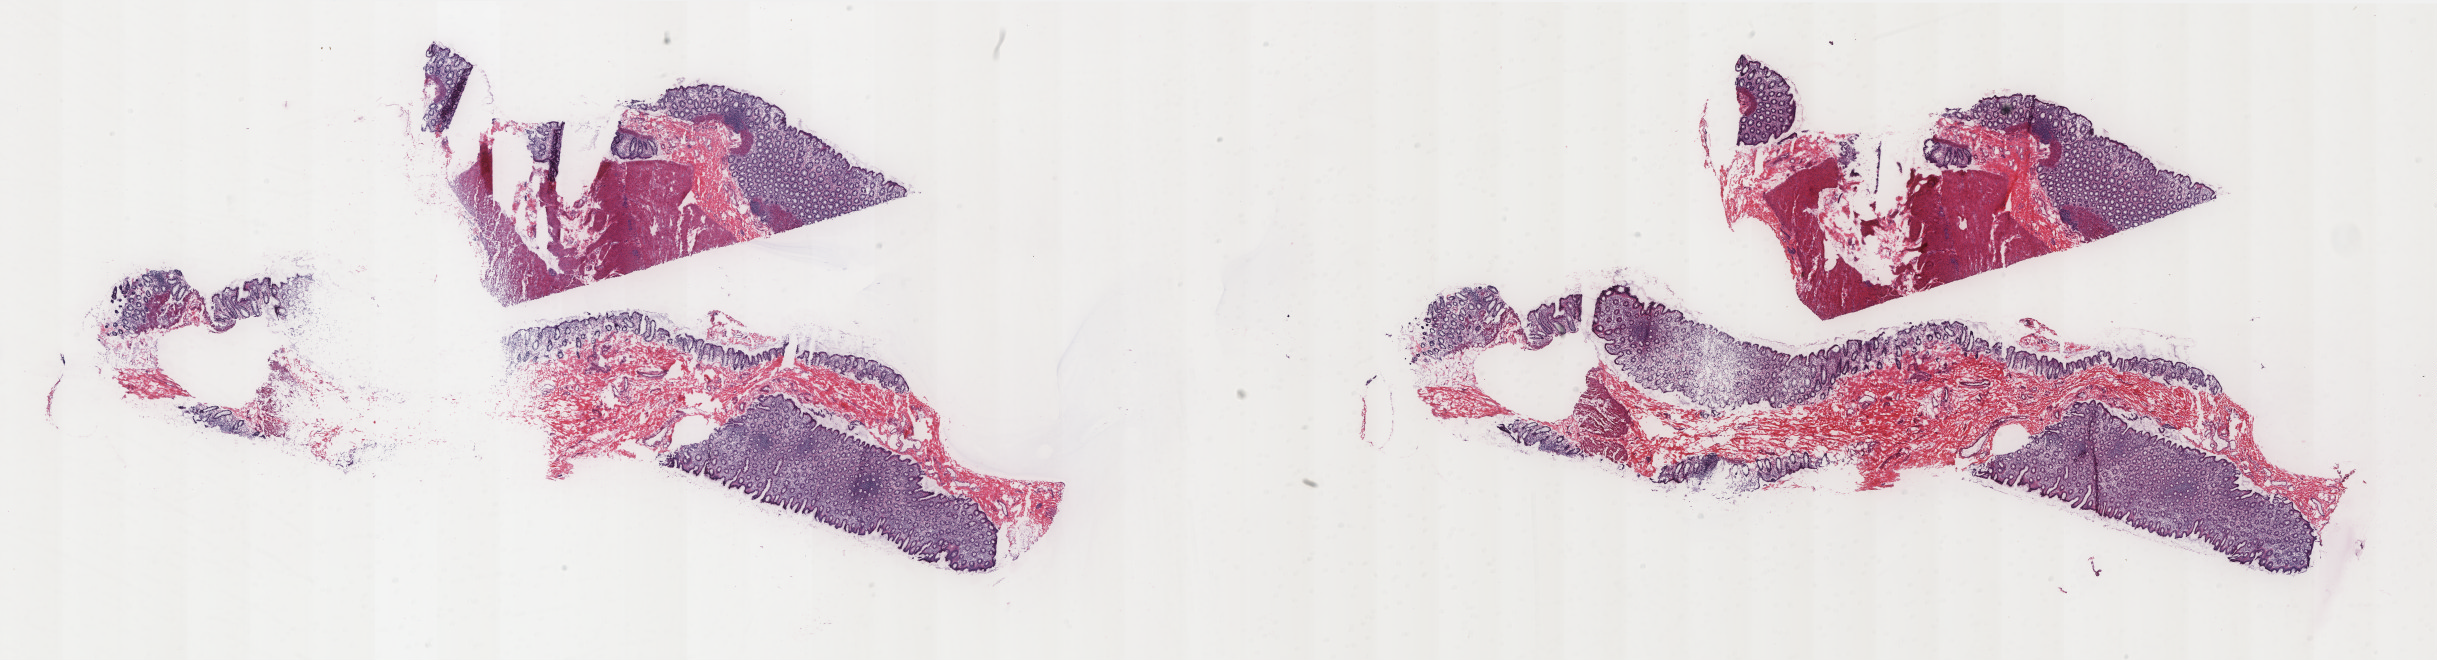
Digitized H&E tissue section (whole slide), a low-resolution overview of the entire scanned area, about 38.9 x 10.5 mm (slide scanned at 20x), frozen section, rectum, solid tissue normal (non-tumour tissue) sample. Female, age 49 years at initial diagnosis. Pathologist review of this section (percent, as recorded): tumour cells 0%, normal cells 100%. Inflammatory infiltration, as recorded: lymphocyte infiltration 40%, monocyte infiltration 7%, neutrophil infiltration 0%.
- this section: solid tissue normal sample (biorepository sample class)
- patient diagnosis: Adenocarcinoma, NOS